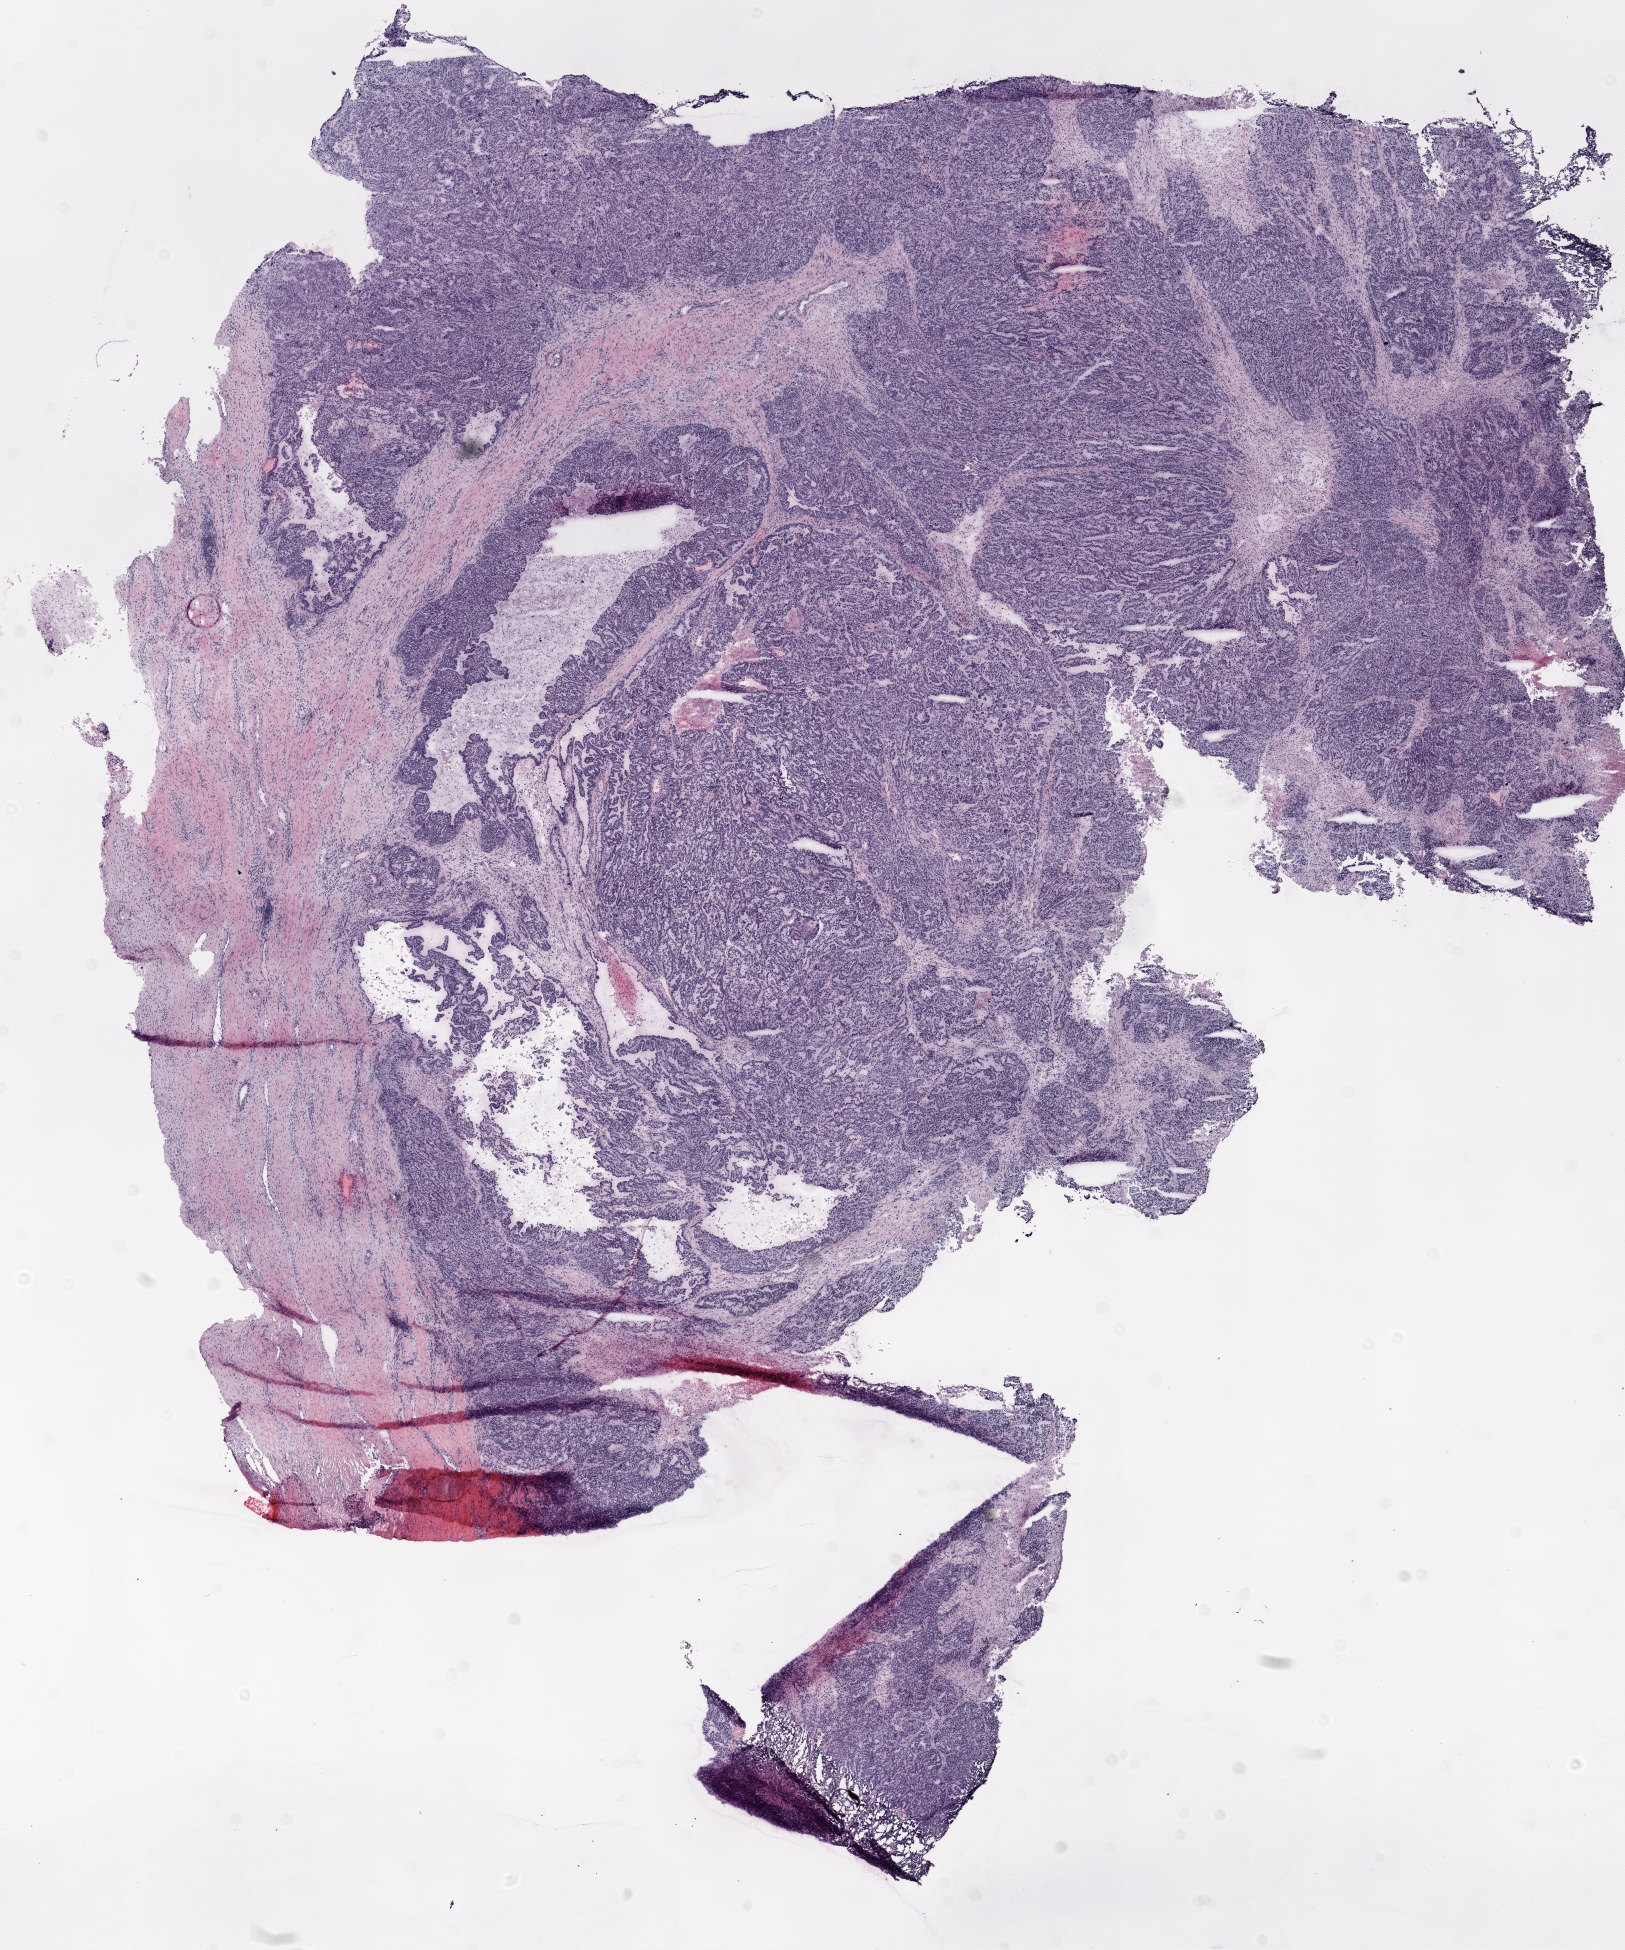
H&E whole-slide image, low-resolution overview of the scanned area, about 13.0 x 15.6 mm, frozen section, sample: primary tumour, ovary. Female patient; age at initial diagnosis 59 years. Histologic grade: G3 (poorly differentiated). Slide review estimates, as recorded: tumour cells 70%, tumour nuclei 70%, normal cells 0%, stromal cells 30%, necrosis 0%. Infiltration values recorded for this section: lymphocyte infiltration 0%, monocyte infiltration 0%, neutrophil infiltration 0%.
* laterality: right
* histologic diagnosis: Serous cystadenocarcinoma, NOS
* FIGO stage: IIC